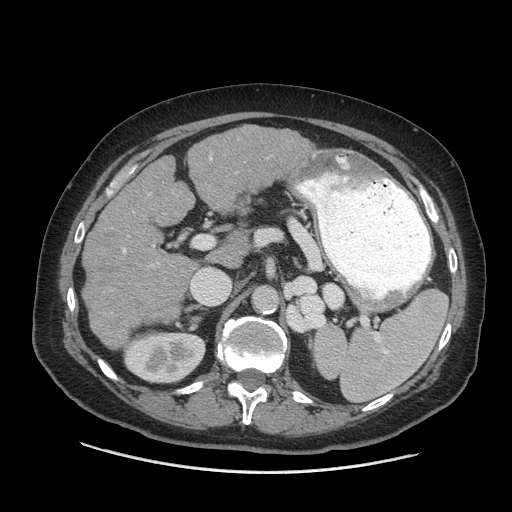
Contrast-enhanced abdominal CT (liver protocol), one axial slice. Position 34 of 77 along the scan axis. 140 kVp. Soft-tissue window (W 400 / L 40 HU). 2.5 mm slice thickness. 512 × 512 image matrix, field of view 420 × 420 mm. Case-level facts recorded for this patient, not image findings: diagnosis: hepatocellular carcinoma (patient treated with transarterial chemoembolisation; whether this scan precedes or follows treatment is not stated here); TNM stage (as recorded): Stage-I; Child-Pugh class: A; tumour size: 3.8 cm.
Outlined on this slice (semi-automatic segmentation, software-assisted and operator-edited):
- liver parenchyma outside the tumour (the mass and vessels are separate outlines, so this box may not span the whole liver): bounding box <82,126,316,348> (left, top, right, bottom; pixels)
- liver vessels: <123,157,212,264>